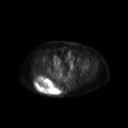
FDG PET of an extremity soft-tissue mass (from a PET/CT study), one axial slice. Position 62 of 267 along the scan axis. 3.27 mm slice thickness. 128 × 128 image matrix, field of view 600 × 600 mm. Female patient, age 60 years. Case-level facts recorded for this patient, not image findings: histological type: spindle cell suggestive of myxofibrosarcoma; grade: intermediate; site of the primary tumour: right buttock.
Structures marked on this image (expert contour drawn on MRI and transferred to this co-registered scan by the dataset authors):
- gross tumour volume (mass): box from (x=35, y=77) to (x=61, y=95) px